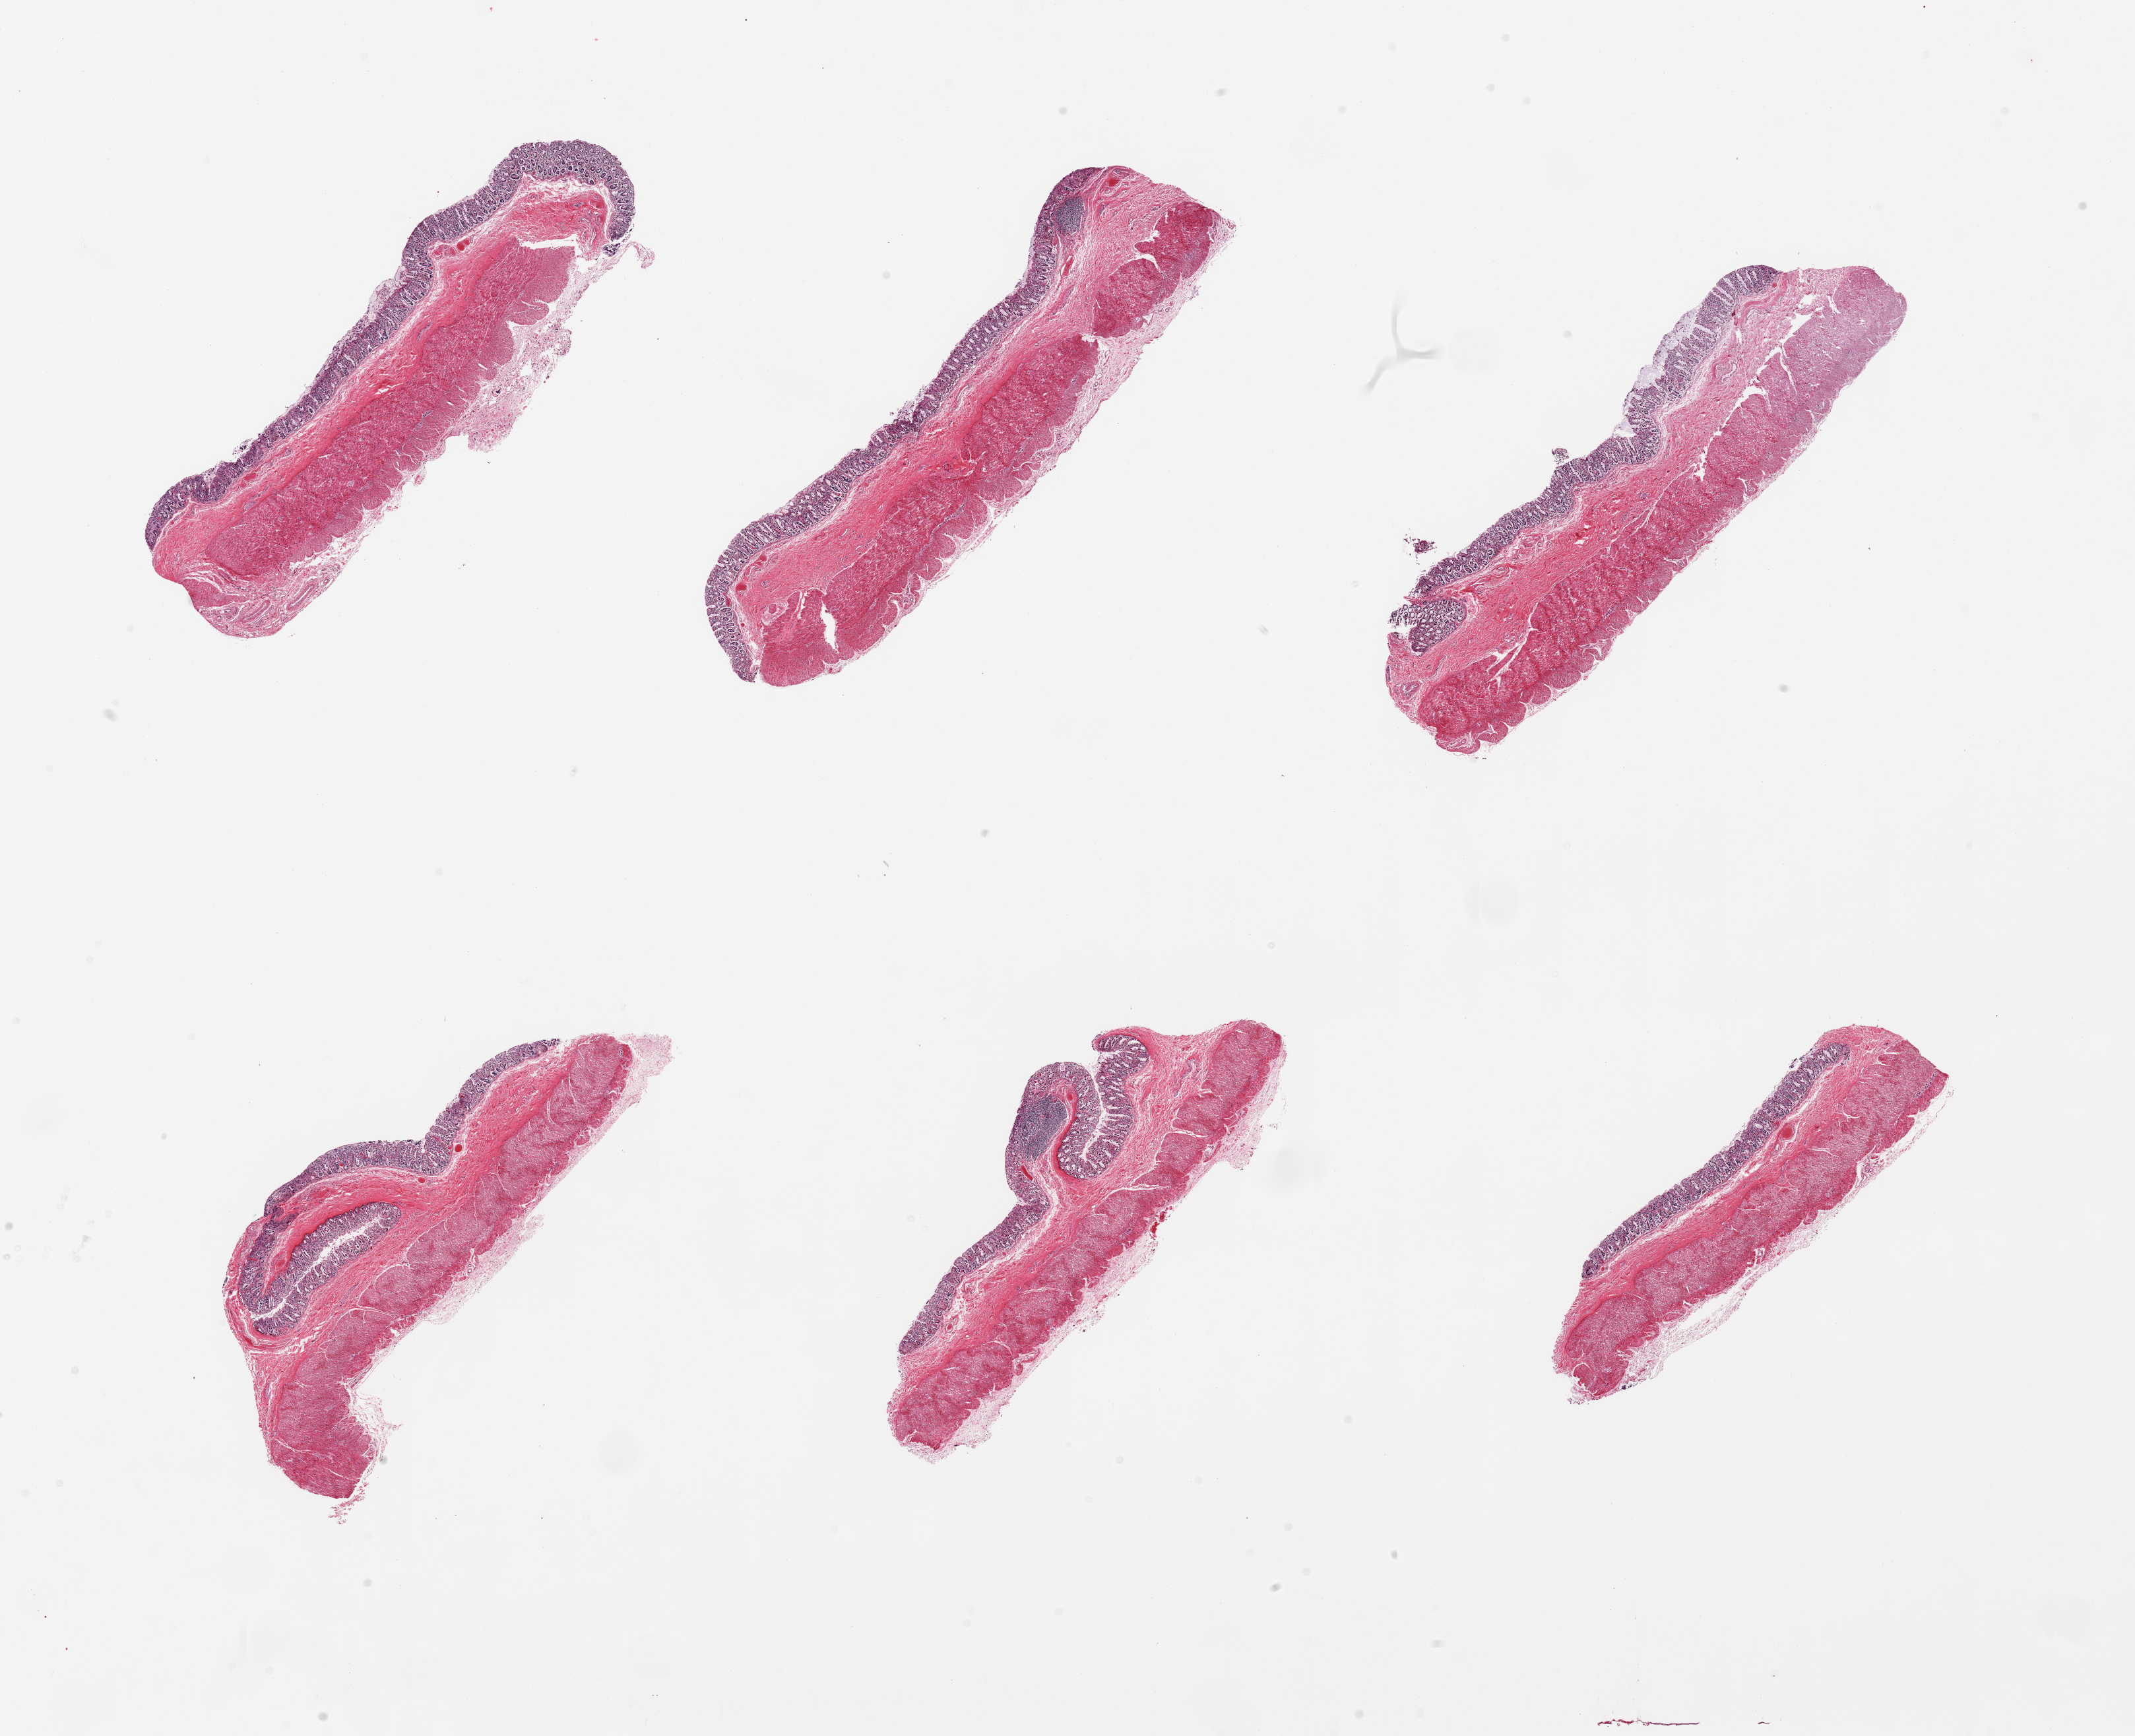
H&E whole-slide image, brightfield — low-resolution overview of the scanned area, about 25.6 x 20.8 mm; PAXgene-fixed, paraffin-embedded tissue; section of transverse colon (target tissue); donor tissue sample. Donor: male.
- pathologist's review note for this sample: 6 pieces; mucosa largely autpolyzed